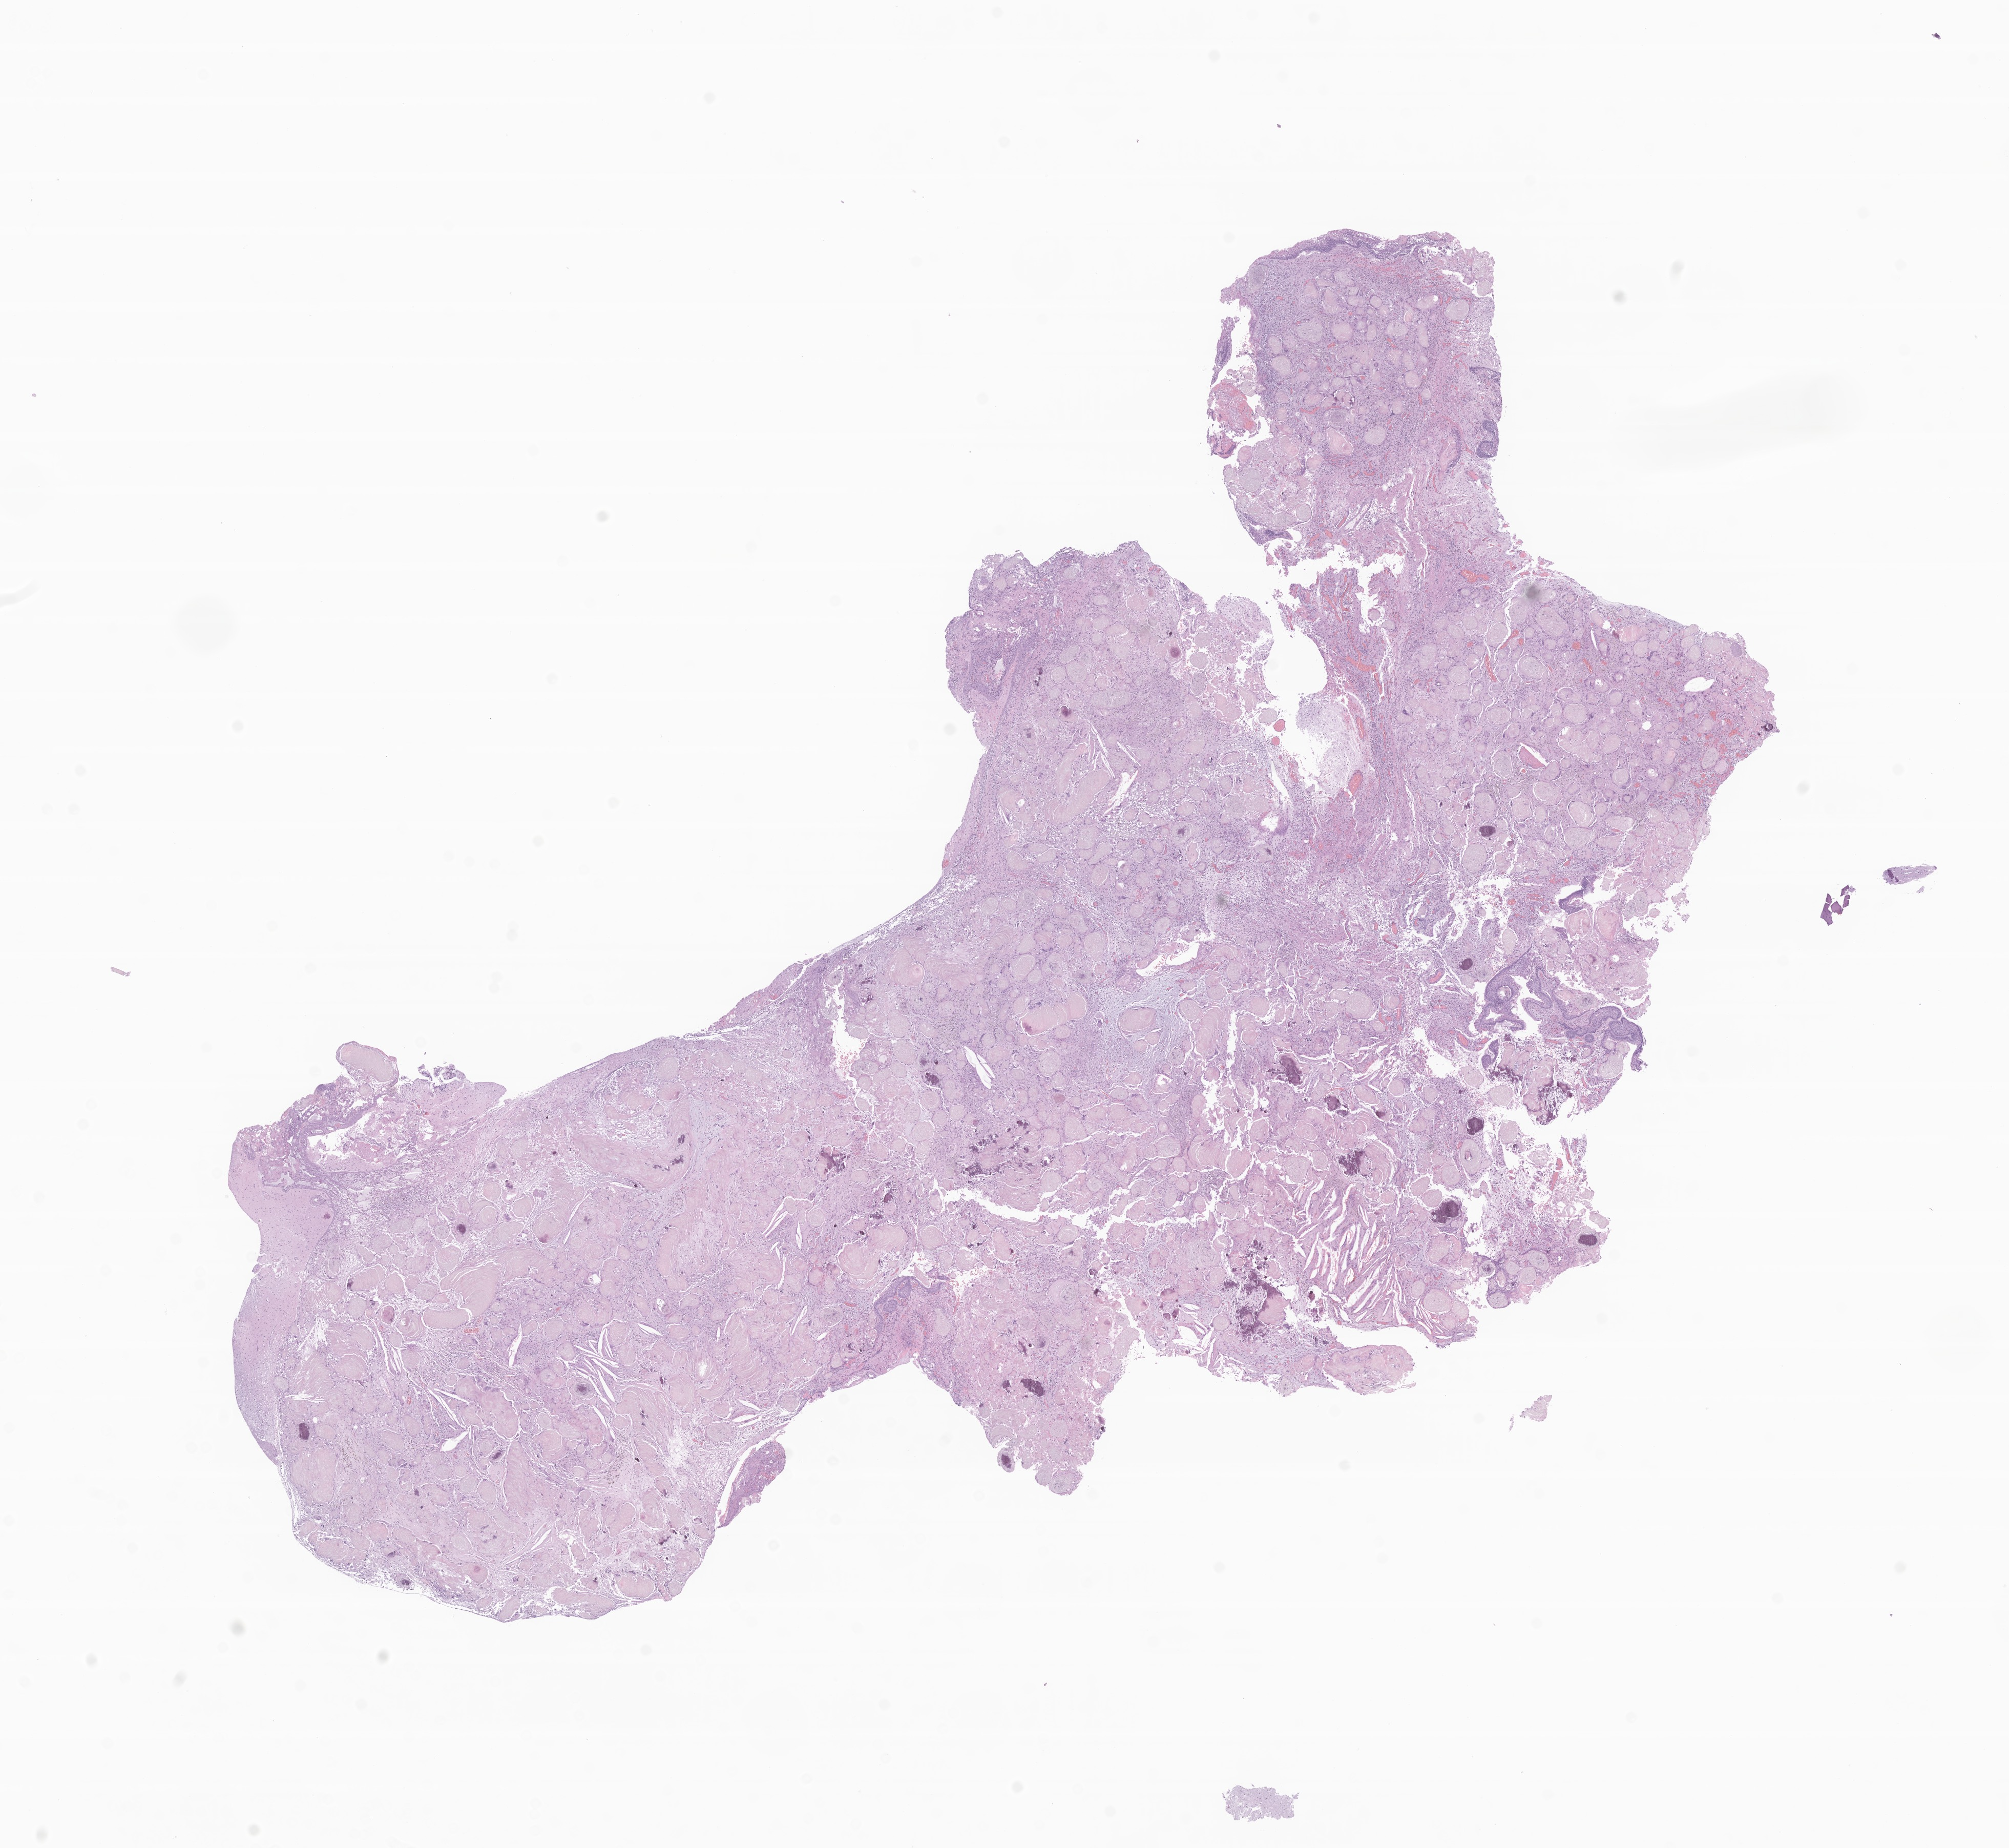
Whole-slide image, hematoxylin and eosin (H&E) stain of tumor tissue from the brain — low-resolution overview of the scanned area, about 16.5 x 15.2 mm, FFPE section. Patient: male, age 151 months (12 years 7 months).
Recorded diagnosis: Craniopharyngioma, adamantinomatous.